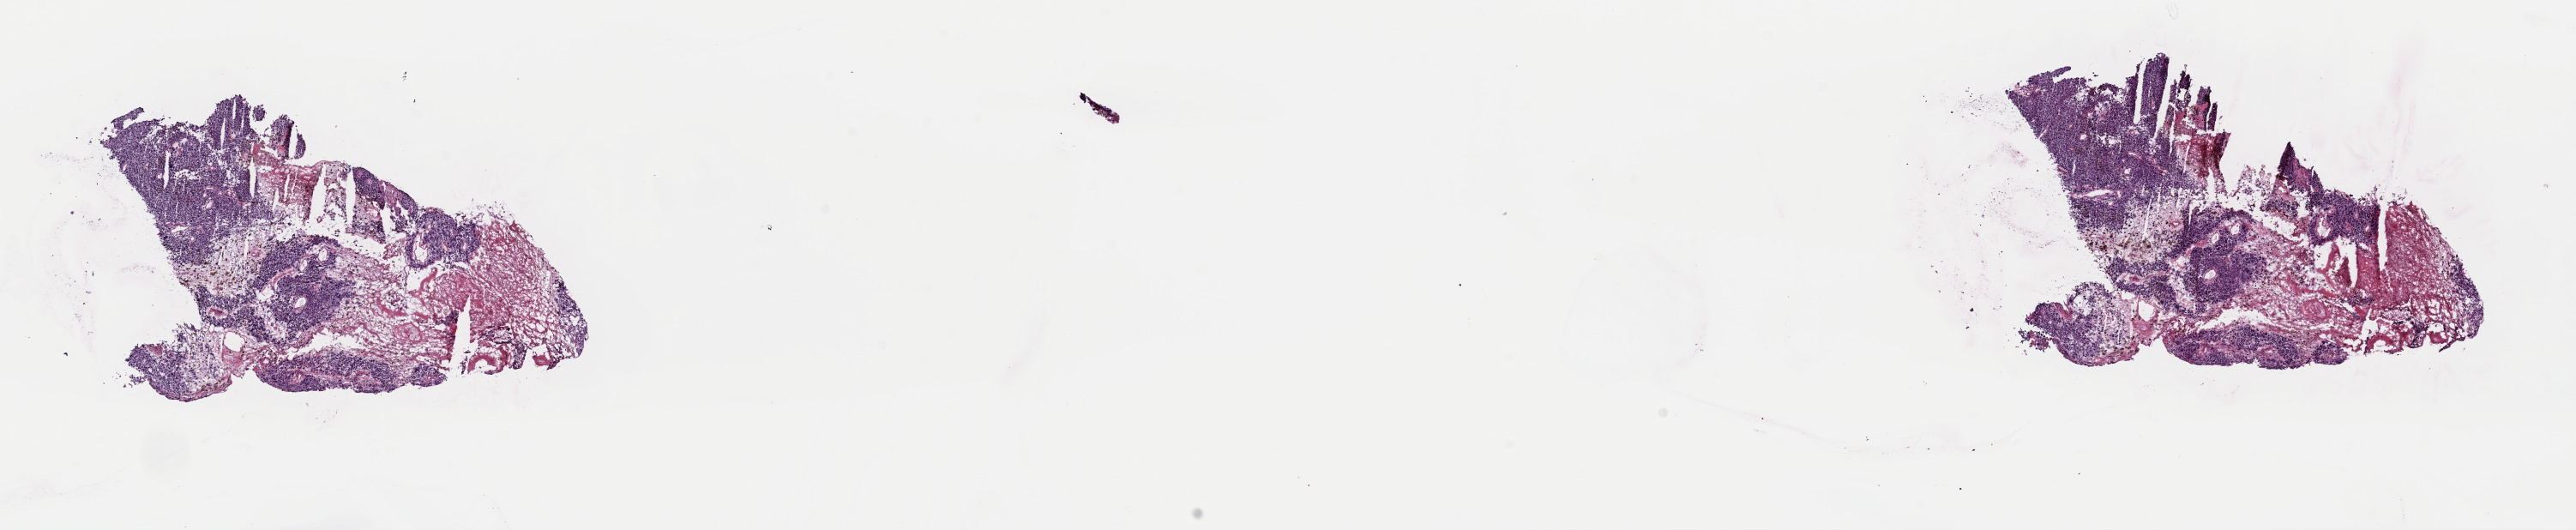
H&E-stained whole-slide image, low-resolution overview of the scanned area, about 23.7 x 4.9 mm, frozen section from the top of the tissue portion, primary tumour sample from the skin. Patient: male, age at initial diagnosis 68 years. Pathologist review of this section (percent, as recorded): tumour cells 80%, tumour nuclei 90%.
Pathologic diagnosis: Malignant melanoma, NOS.